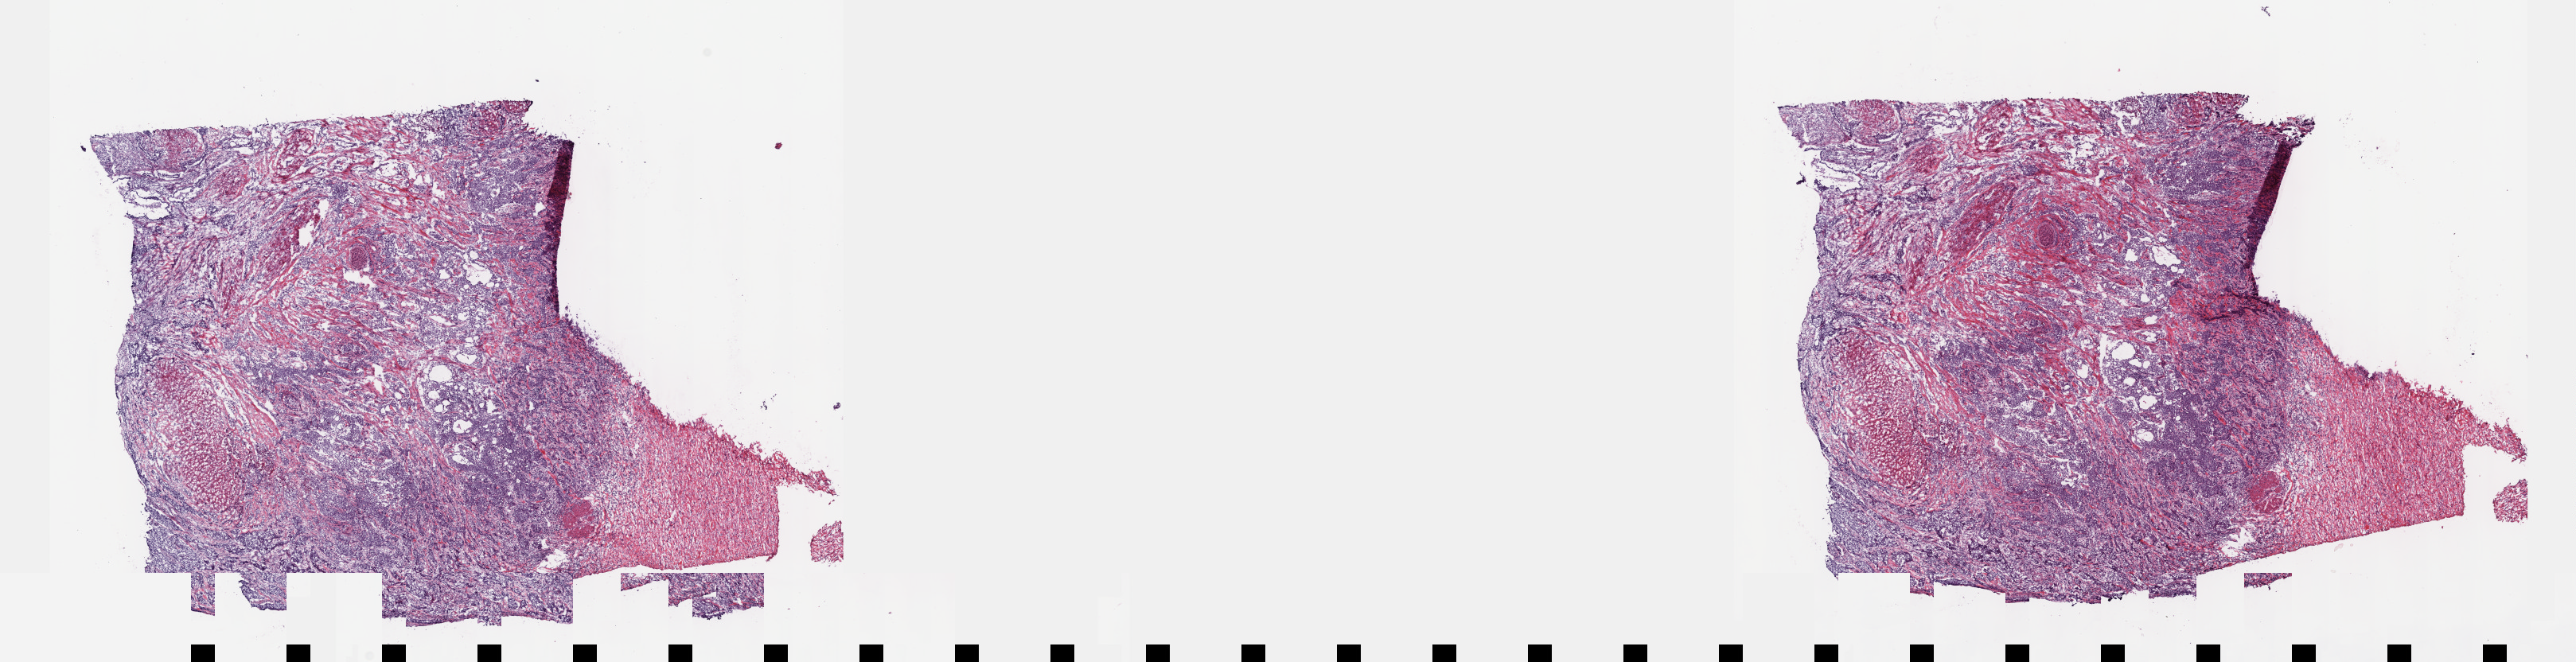
Whole-slide histology image, H&E-stained — shown as a low-resolution overview of the whole scanned area (about 26.2 x 6.7 mm, slide scanned at 40x), frozen section, primary tumour sample from the bladder. Male, age 77 years at initial diagnosis. Histologic grade: high grade. Slide review estimates, as recorded: tumour cells 95%, tumour nuclei 75%, normal cells 5%, stromal cells 0%, necrosis 0%. Inflammatory infiltration, as recorded: lymphocyte infiltration 4%, monocyte infiltration 0%, neutrophil infiltration 0%.
AJCC pathologic stage: III. Histologic diagnosis: Transitional cell carcinoma (anterior wall of bladder).